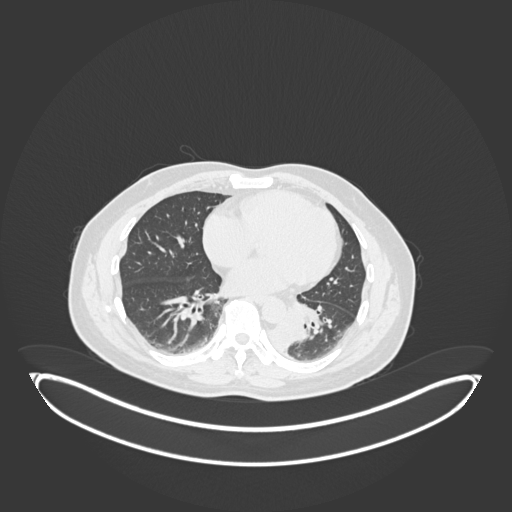
Chest CT, one axial slice. Slice 72 of 258 in the series (ordered by position). 120 kVp. Lung window (W 1500 / L -600 HU). 512 × 512 image matrix. Male patient, age 54 years. Case-level facts recorded for this patient, not image findings: clinical TNM (as recorded): T3 N0 M0.
Outlined on this slice (bounding box drawn by a radiologist):
- lung tumour (recorded histology: squamous cell carcinoma): box from (x=269, y=315) to (x=309, y=358) px